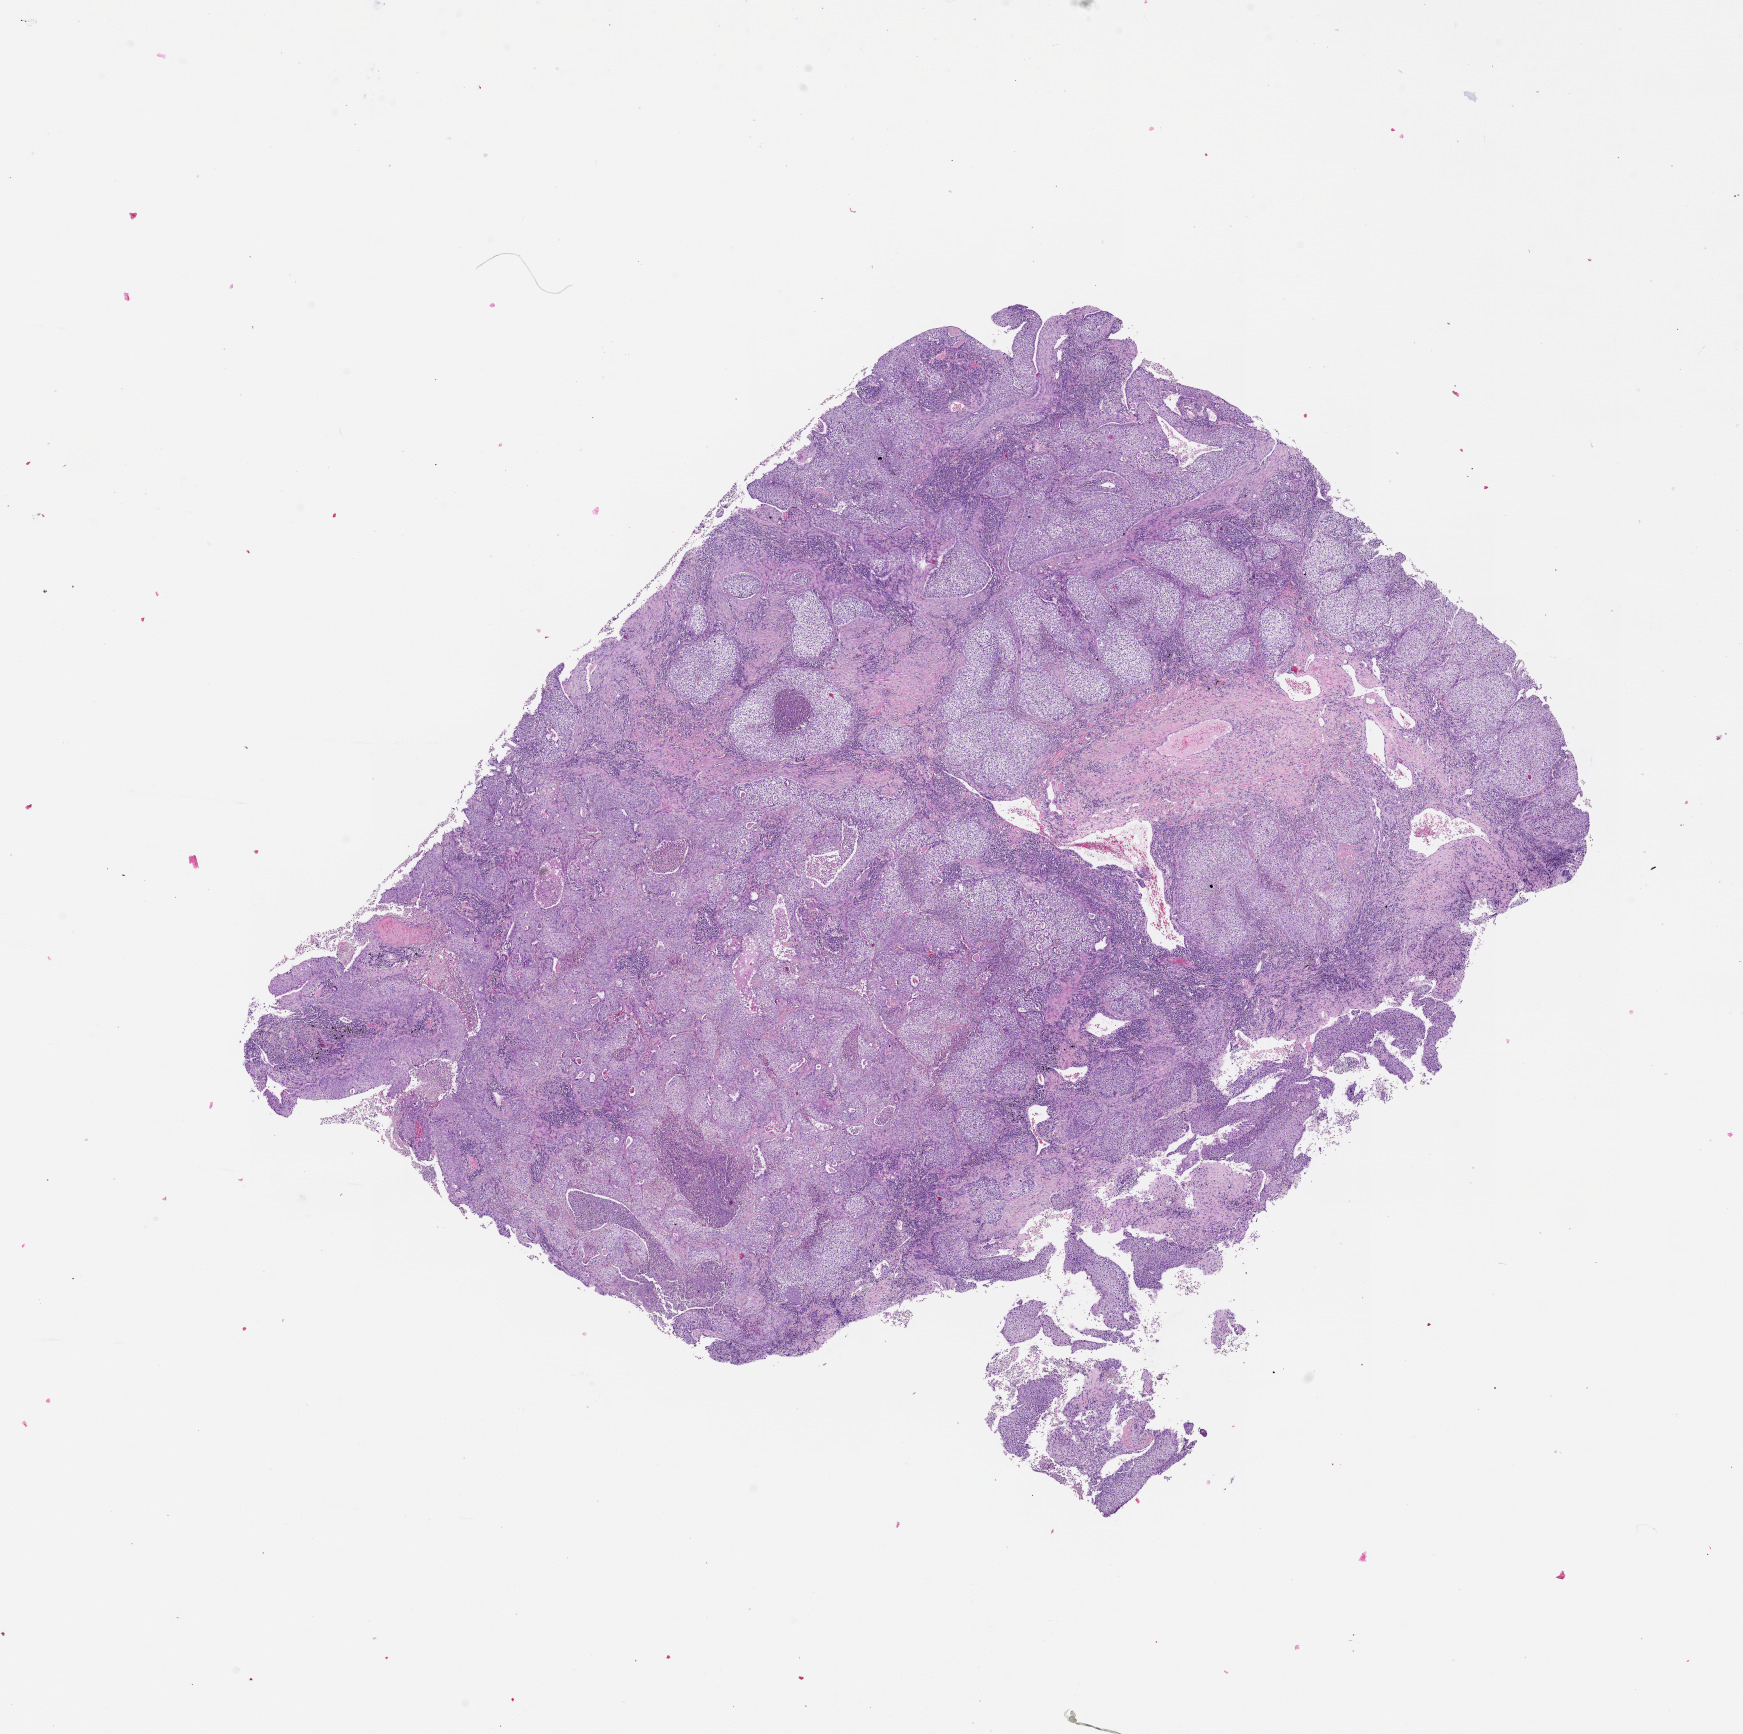
Hematoxylin and eosin (H&E) stained whole-slide image — shown as a low-resolution overview of the whole scanned area (about 14.0 x 14.0 mm); lung, tumour tissue. 60-year-old male patient.
- patient diagnosis (cohort enrolment): squamous cell carcinoma (lung)